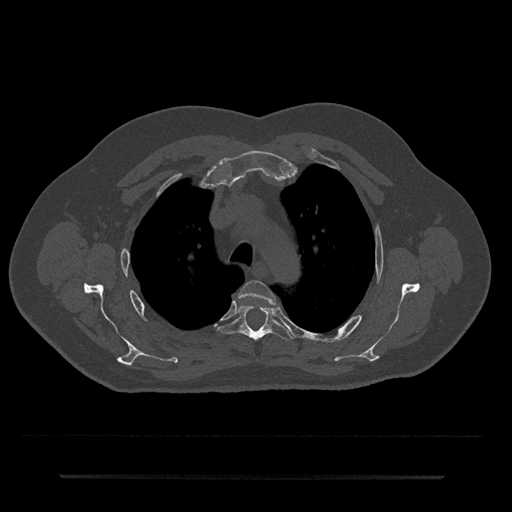
CT including the spine, one axial slice. Bone window (W 1800 / L 400 HU). 0.5 mm slice thickness. 512 × 512 image matrix, field of view 437 × 437 mm. Male patient, age 69 years. Case-level facts recorded for this patient, not image findings: primary cancer: prostate.
Structures marked on this image (semi-automatically segmented with operator editing):
- T3 vertebra: box from (x=239, y=280) to (x=275, y=305) px
- T4 vertebra: (x=218, y=305)–(x=293, y=341)